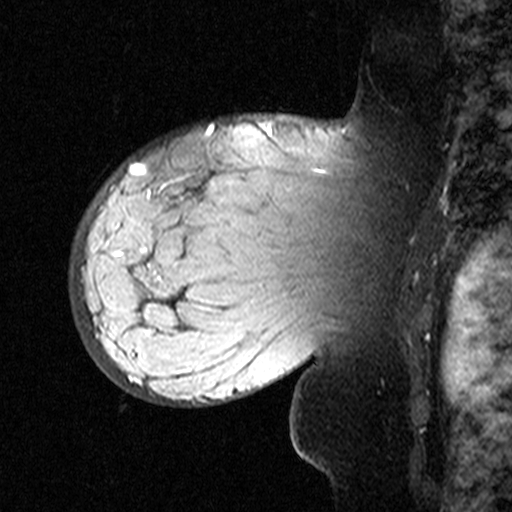
Breast MRI (dynamic contrast-enhanced), one sagittal slice. Position 34 of 44 along the scan axis. Dynamic contrast-enhanced study with each time point stored as its own series, time point 2 of 3 at this slice position (early post-contrast, ordered by acquisition time). 1.5 T. TE 4.5 ms, TR 11 ms. 512 × 512 image matrix, field of view 200 × 200 mm. Female patient, age 53 years. Case-level facts recorded for this patient, not image findings: setting: breast cancer imaged before/during neoadjuvant chemotherapy; receptor status: HR-positive, HER2-negative.
Annotated regions visible in this slice (semi-automatically segmented with operator editing):
- analysis volume of interest (the breast-tissue region the enhancement analysis was run in; not a lesion): bounding box [x1, y1, x2, y2] px = [76, 140, 311, 353]
- tumour enhancement mask (voxels above the 90 % enhancement threshold inside the analysis volume of interest): [117, 253, 154, 333]